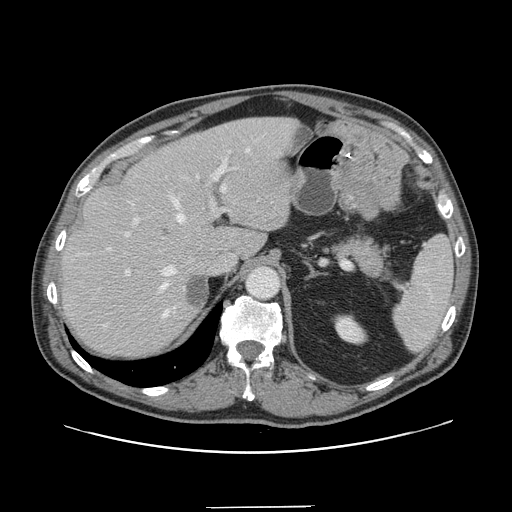
Contrast-enhanced abdominal CT, one axial slice. Slice 105 of 139 in the series (ordered by position). 120 kVp. Soft-tissue window (W 400 / L 40 HU). 2.5 mm slice thickness. 512 × 512 image matrix. Male patient, age 64 years. From the clinical record (not read from this slice): diagnosis: colorectal cancer liver metastases, imaged before liver resection; multiple liver metastases: yes; largest metastasis: 3.5 cm; disease in both lobes: yes.
Structures marked on this image (outlined manually by an expert reader):
- hepatic veins: bounding box [x1, y1, x2, y2] px = [107, 148, 250, 318]
- liver: [62, 118, 296, 355]
- planned liver remnant (the part of the liver to remain after resection): [62, 119, 274, 356]
- portal vein (with intrahepatic branches): [125, 150, 231, 276]
- liver metastasis: [186, 276, 207, 309]